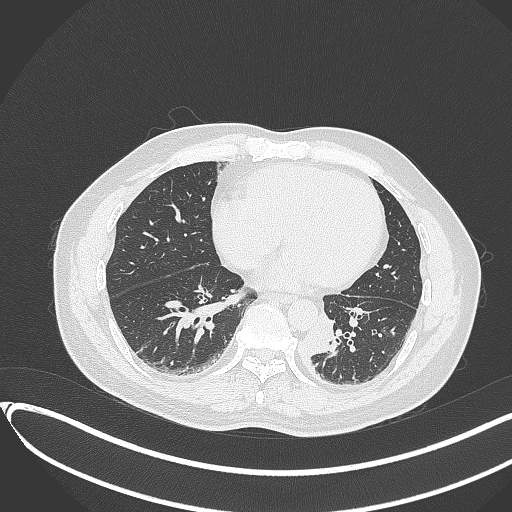
Chest CT, one axial slice. Slice 120 of 417 in the series (ordered by position). 120 kVp. Lung window (W 1500 / L -600 HU). 1 mm slice thickness. 512 × 512 image matrix. Patient: male, 54 years. Case-level facts recorded for this patient, not image findings: clinical TNM (as recorded): T3 N0 M0.
Structures marked on this image (rectangle marked by the reading radiologist):
- lung tumour (recorded histology: squamous cell carcinoma): box from (x=300, y=307) to (x=337, y=361) px